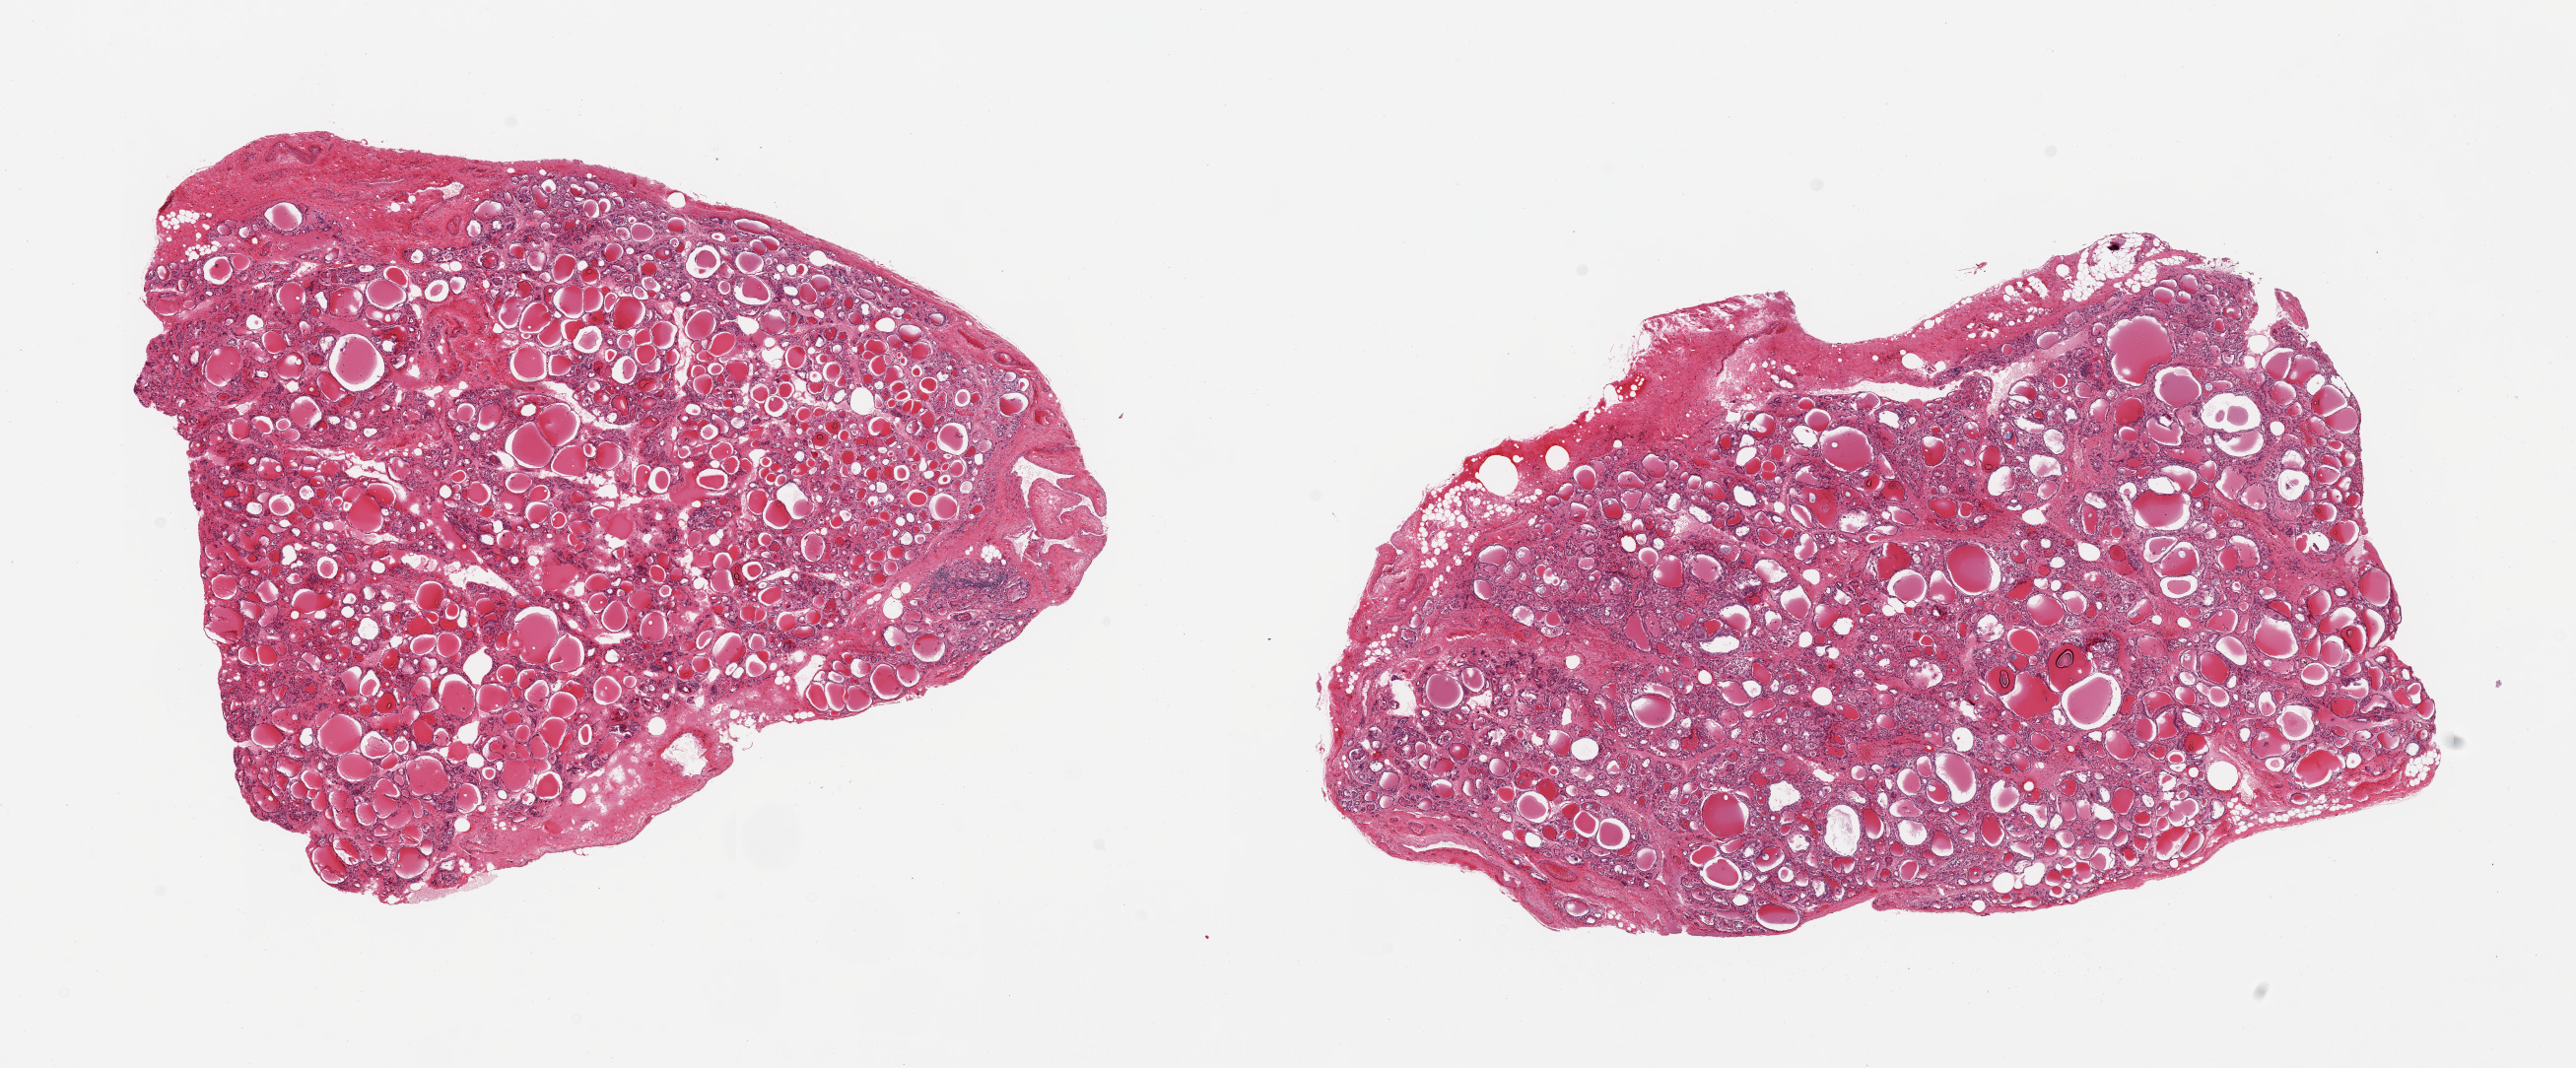
Hematoxylin and eosin (H&E) whole-slide image — a low-resolution overview of the entire scanned area, about 20.7 x 8.6 mm. PAXgene-fixed, paraffin-embedded tissue. Sampled site (target tissue): thyroid. Donor tissue sample.
* reviewer comment on this tissue sample: 2 pieces; small lymphoid focus